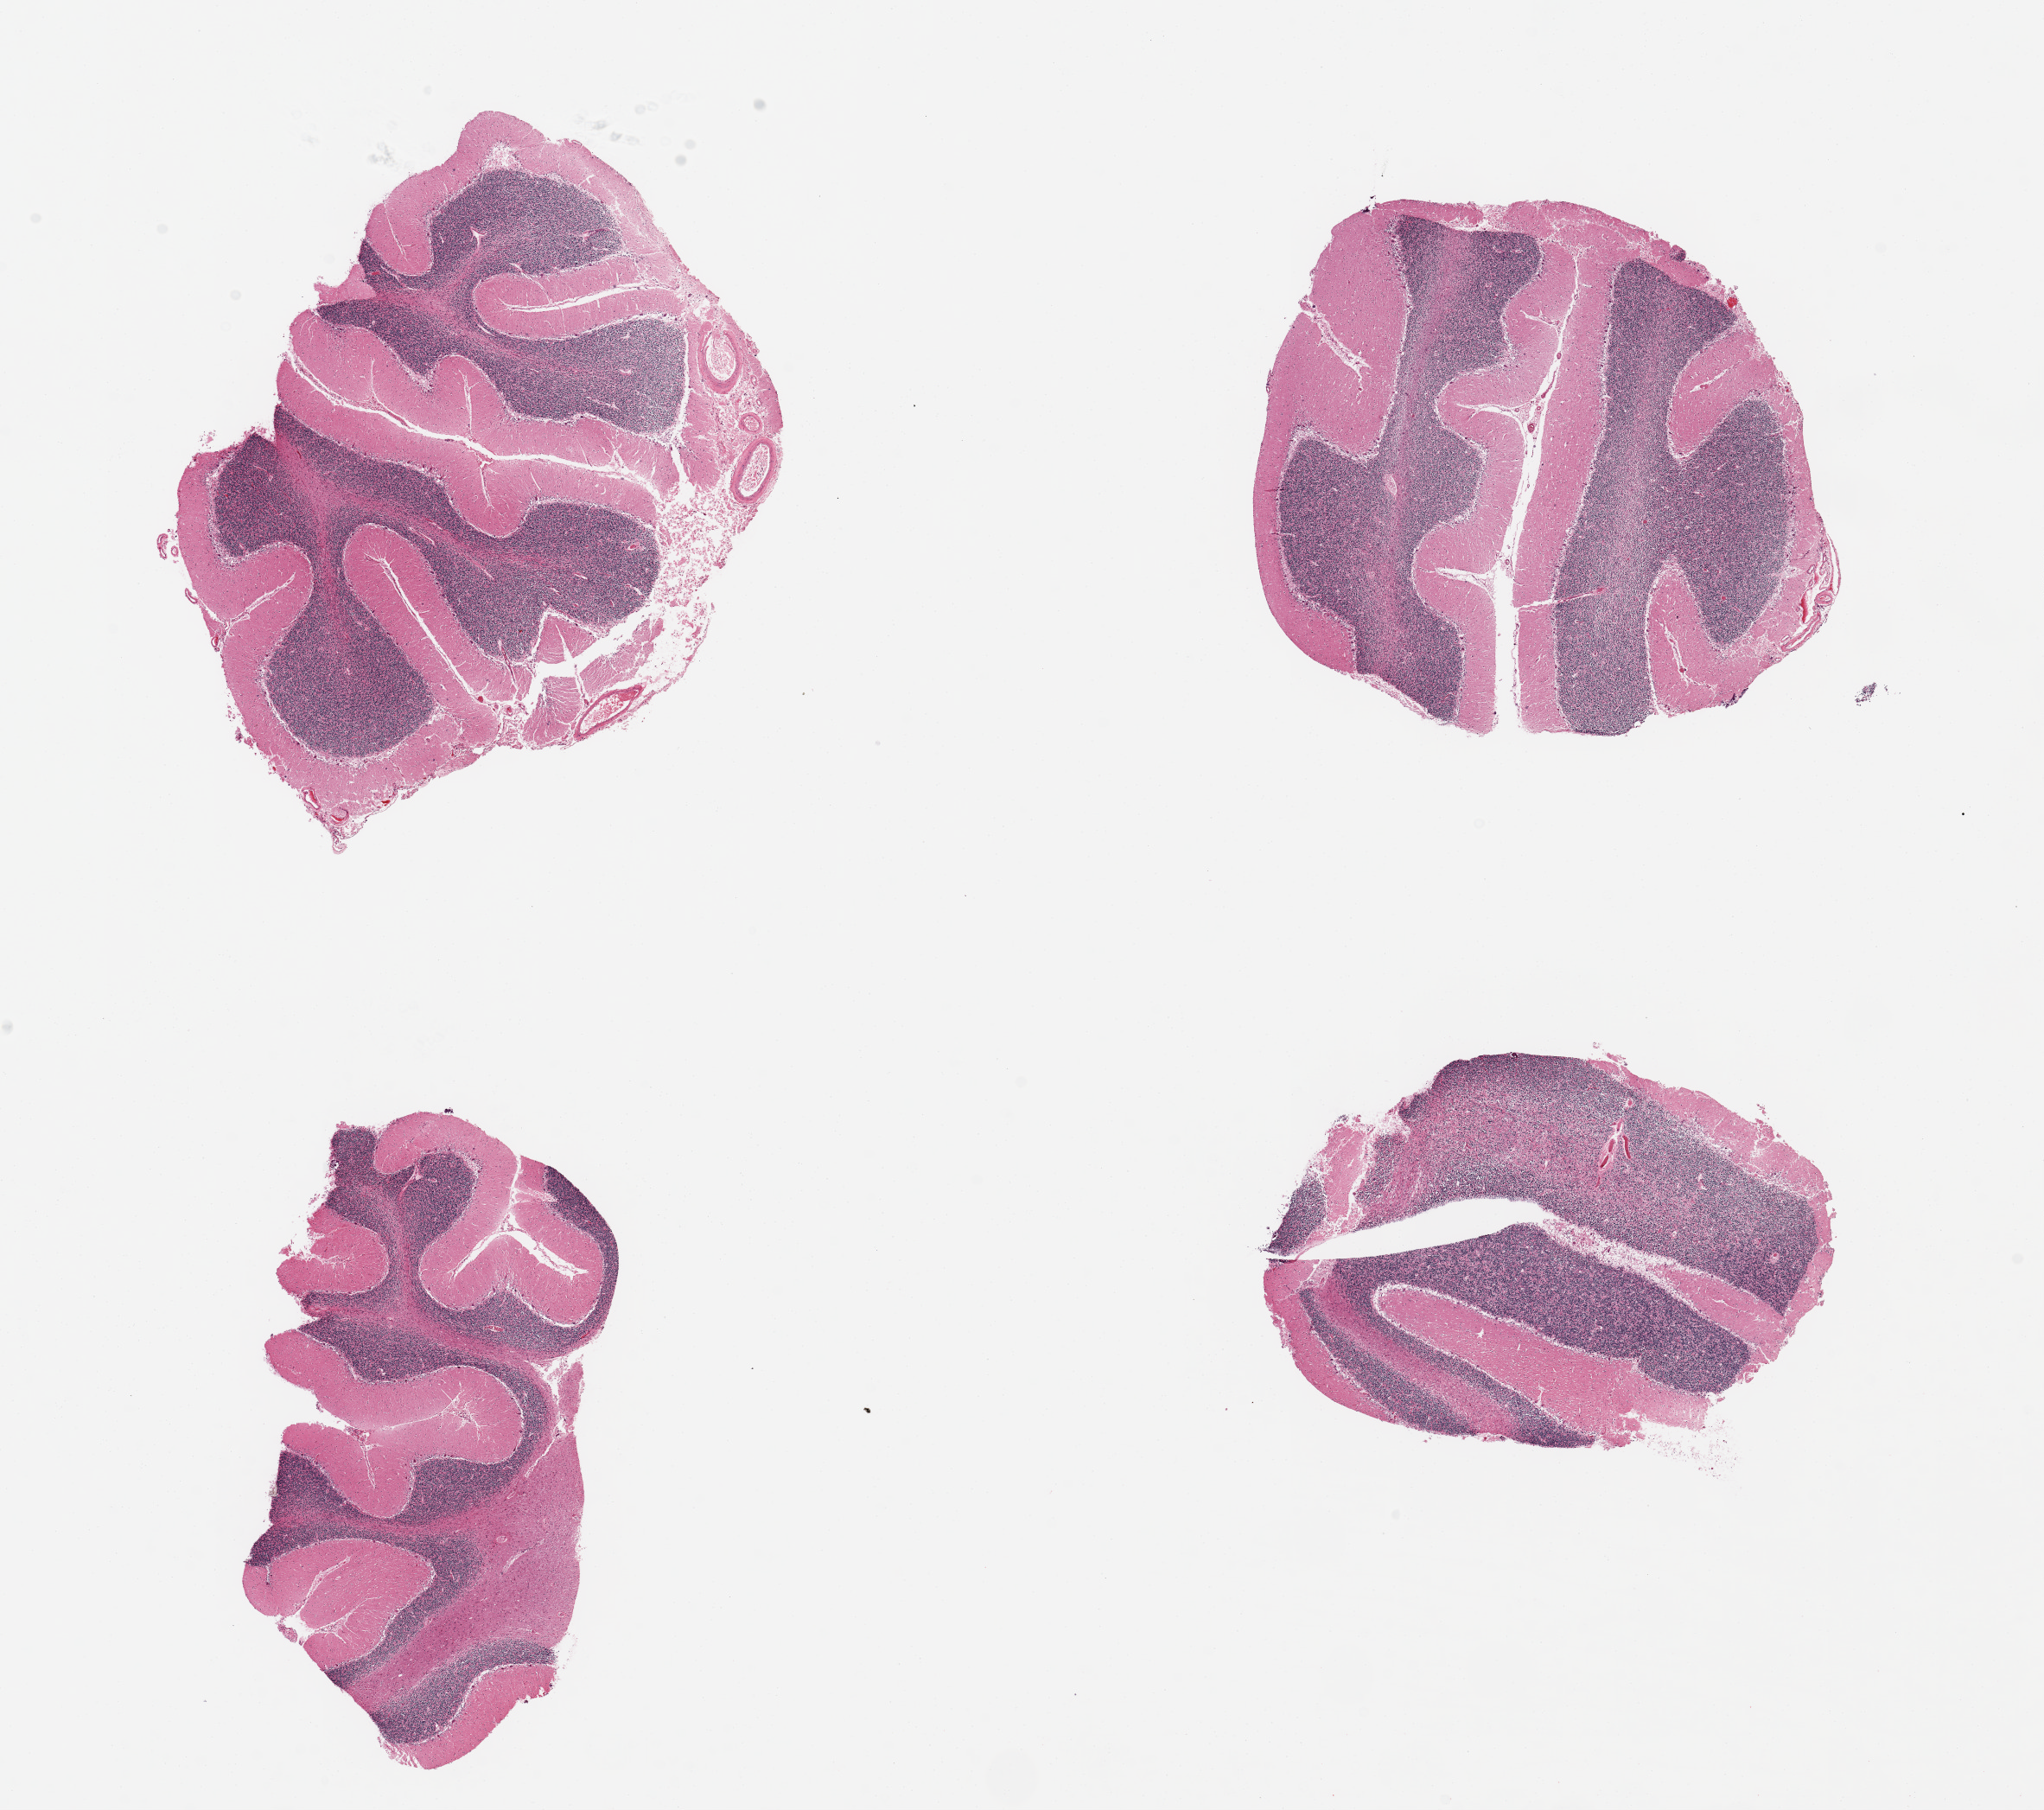
Digitized hematoxylin and eosin (H&E)-stained section — whole scanned area (about 18.7 x 16.6 mm, acquisition: 20x scan) shown as a low-resolution overview; PAXgene-fixed, paraffin-embedded tissue; target tissue: cerebellum; tissue donor sample. Donor sex: female.
* reviewer comment on this tissue sample: 4 ~5x4mm aliquots, granular layer with more autolytic changes